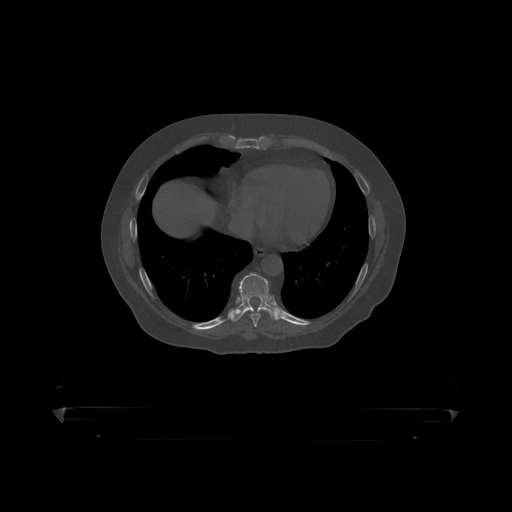
CT including the spine, one axial slice; slice 244 of 390 in the series (ordered by position); reconstruction kernel STANDARD; bone window (W 1800 / L 400 HU); 1.25 mm slice thickness; 512 × 512 image matrix, field of view 650 × 650 mm. Male patient, age 60 years. From the clinical record (not read from this slice): primary cancer: prostate.
Structures marked on this image (semi-automatic segmentation, software-assisted and operator-edited):
- T8 vertebra: bounding box (x1, y1, x2, y2) in pixels: (251, 314, 261, 319)
- T9 vertebra: (232, 273, 276, 317)